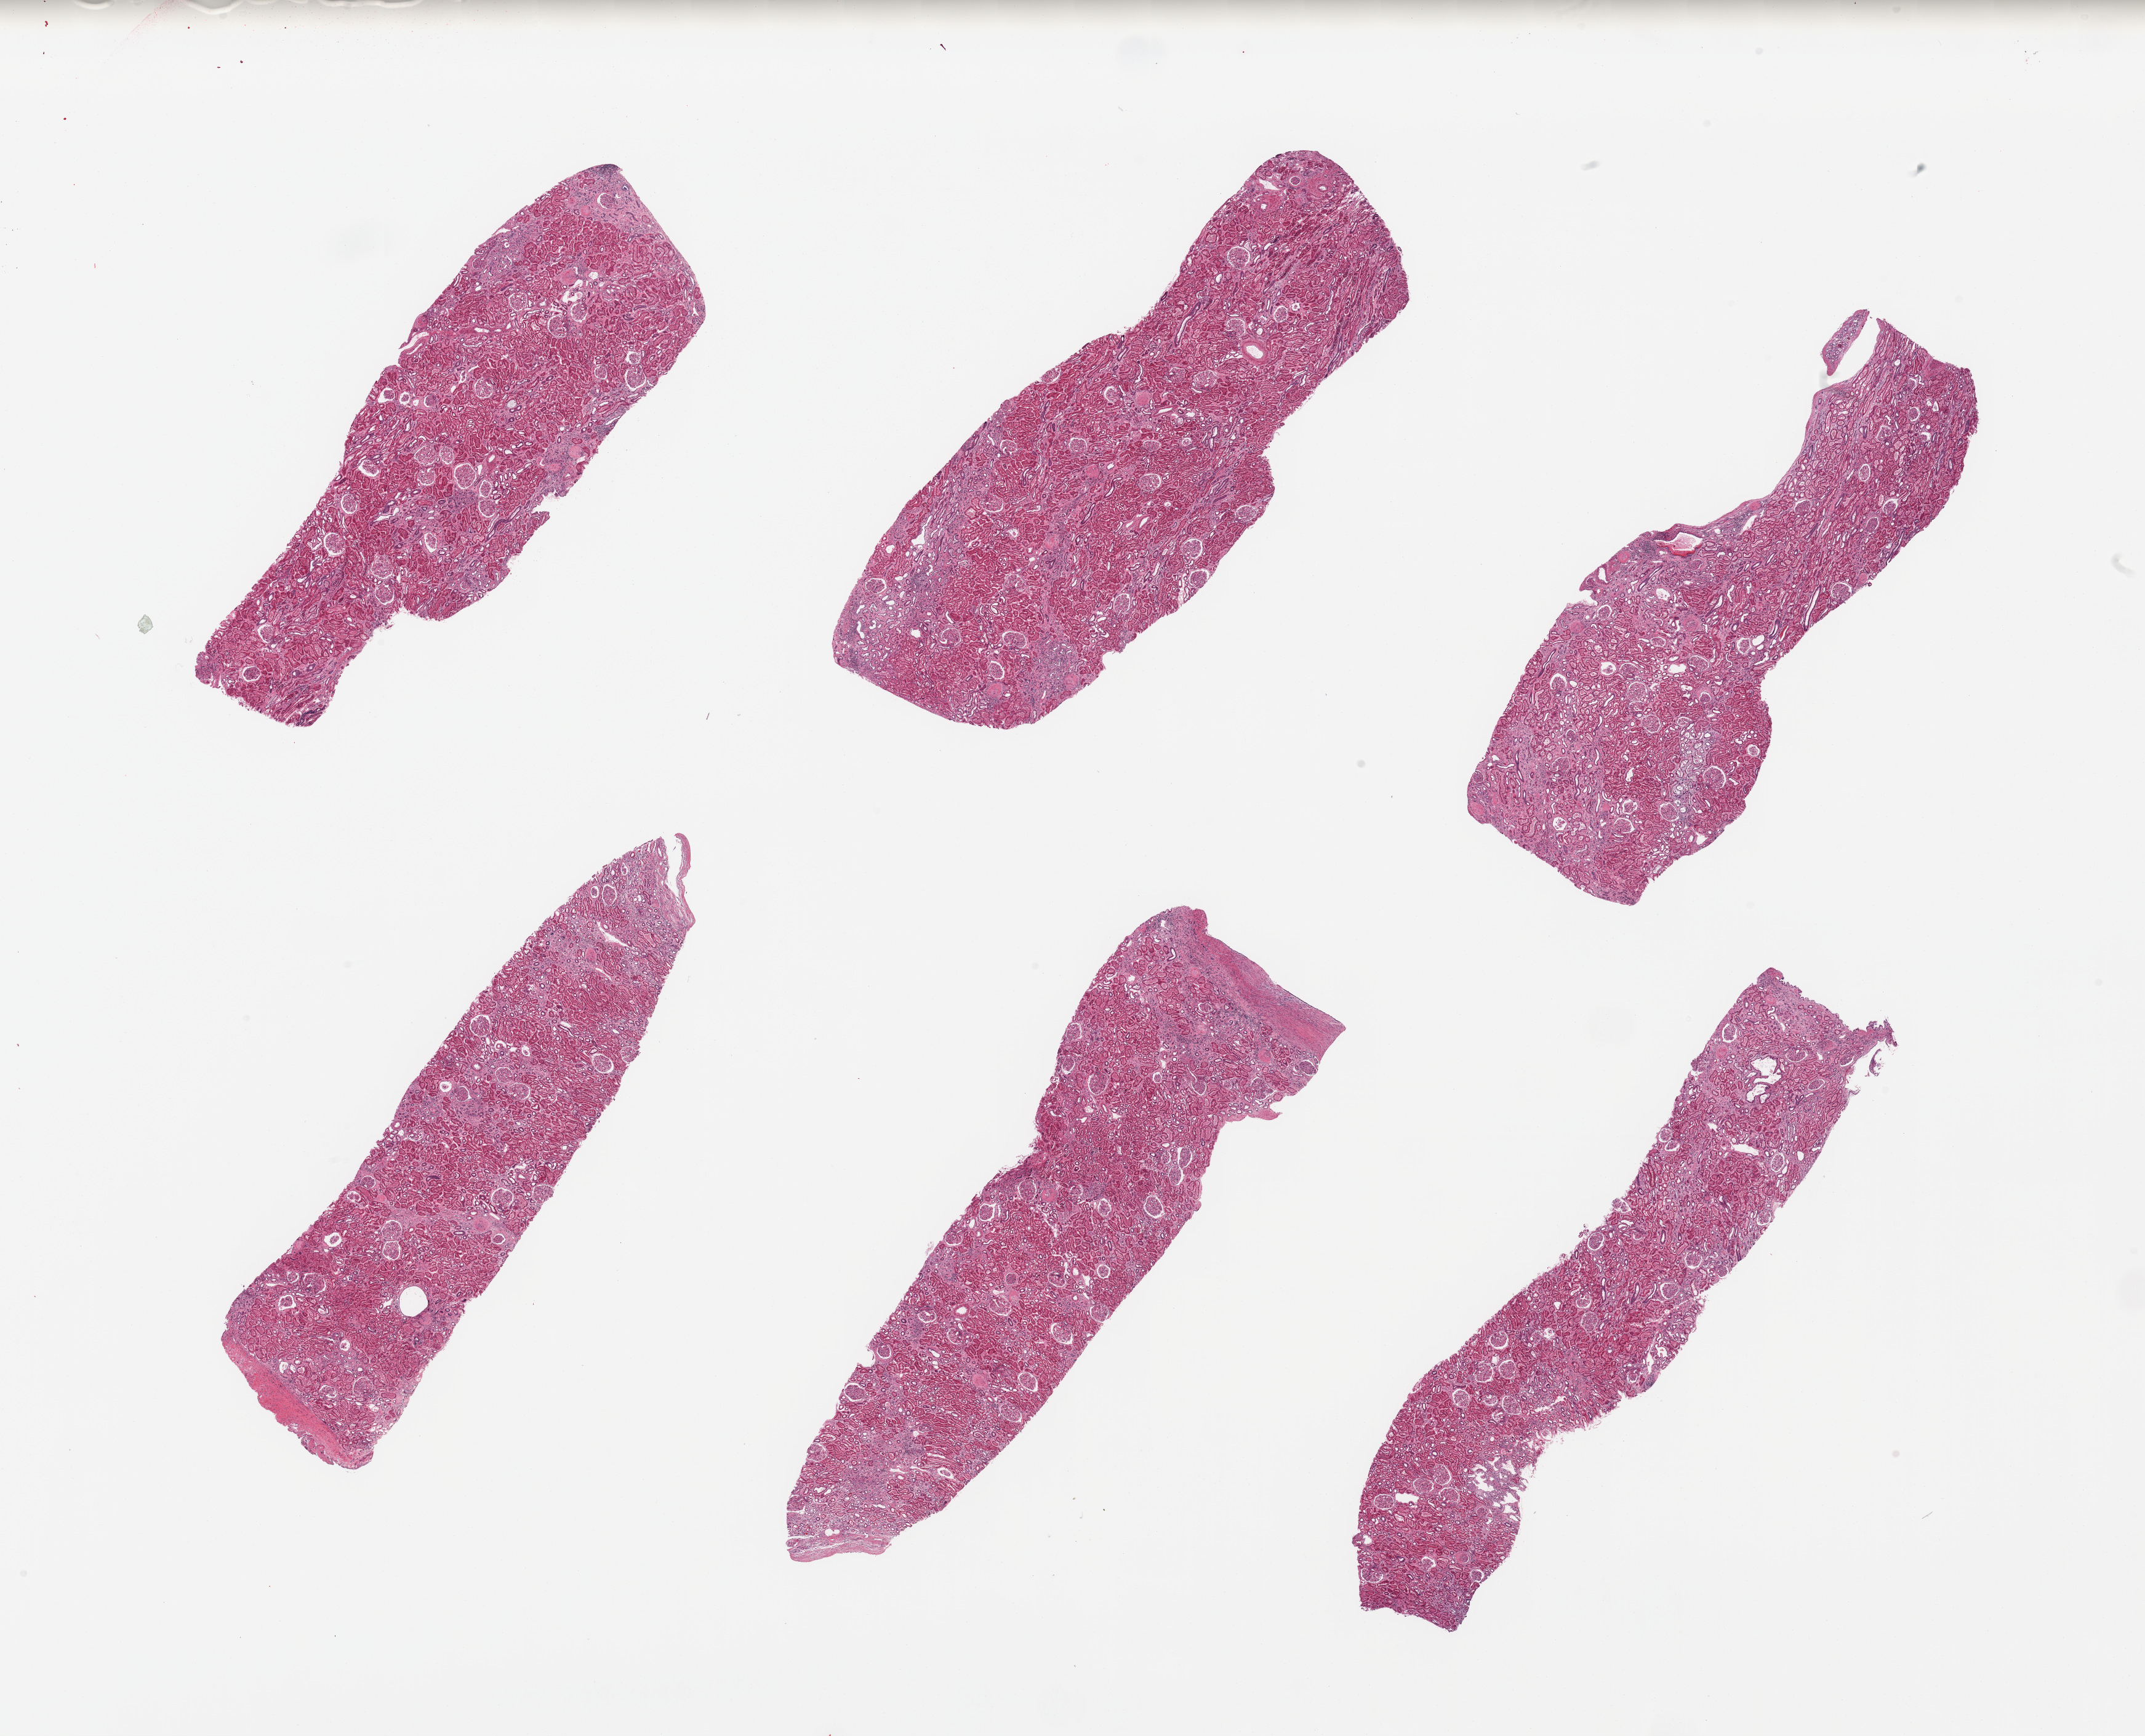
Whole-slide image, hematoxylin and eosin (H&E) stain, shown as a low-resolution overview of the whole scanned area (about 27.6 x 22.3 mm). PAXgene-fixed, paraffin-embedded tissue. Target tissue: renal cortex. Donor tissue sample. Donor: male.
Review note (as recorded): 6 pieces, glomeruli present; patchy chronic interstitial inflammation.